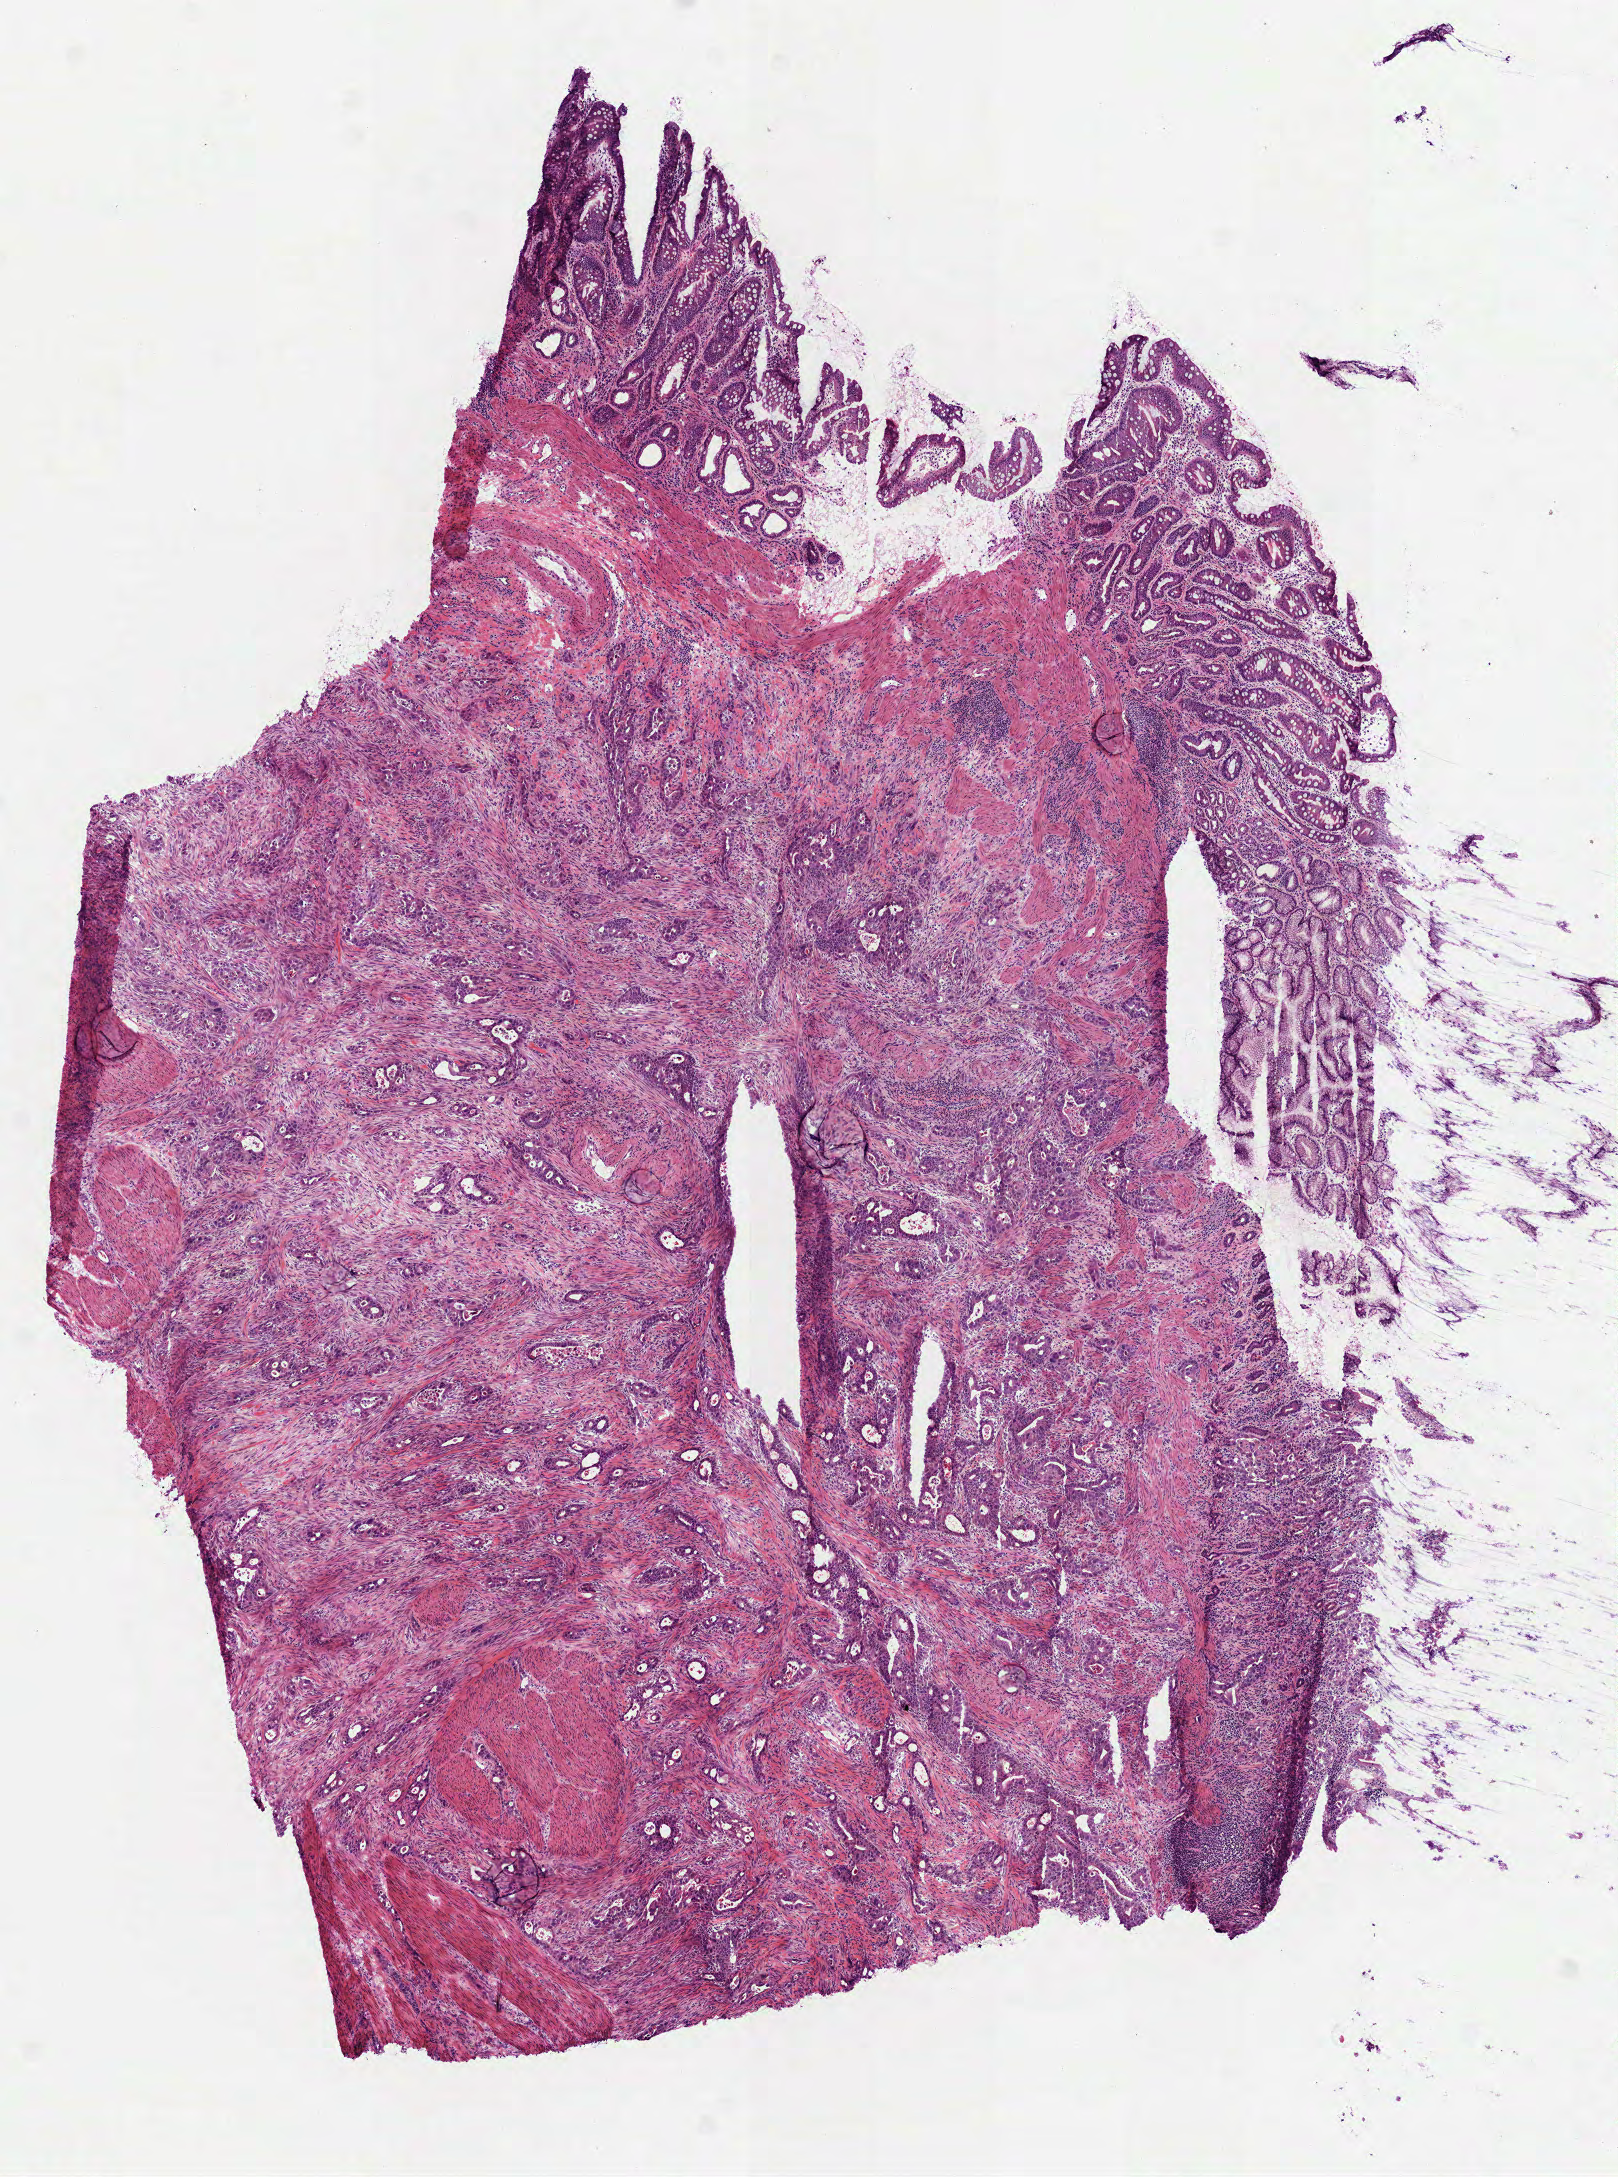
Hematoxylin and eosin (H&E) stained whole-slide image — a low-resolution overview of the entire scanned area, about 6.5 x 8.8 mm, frozen section, stomach, primary tumour sample. Patient: male, age at initial diagnosis 72 years. Histologic grade: G2 (moderately differentiated). Composition of this section per pathologist review: tumour cells 75%, tumour nuclei 62%, normal cells 25%, stromal cells 0%, necrosis 0%. Infiltration values recorded for this section: lymphocyte infiltration 20%, monocyte infiltration 0%, neutrophil infiltration 3%.
AJCC pathologic stage: IB. TNM: T2 N0 M0. Lymph nodes positive (case pathology): 0 of 3 examined. Pathologic diagnosis: Adenocarcinoma, NOS (gastric antrum).